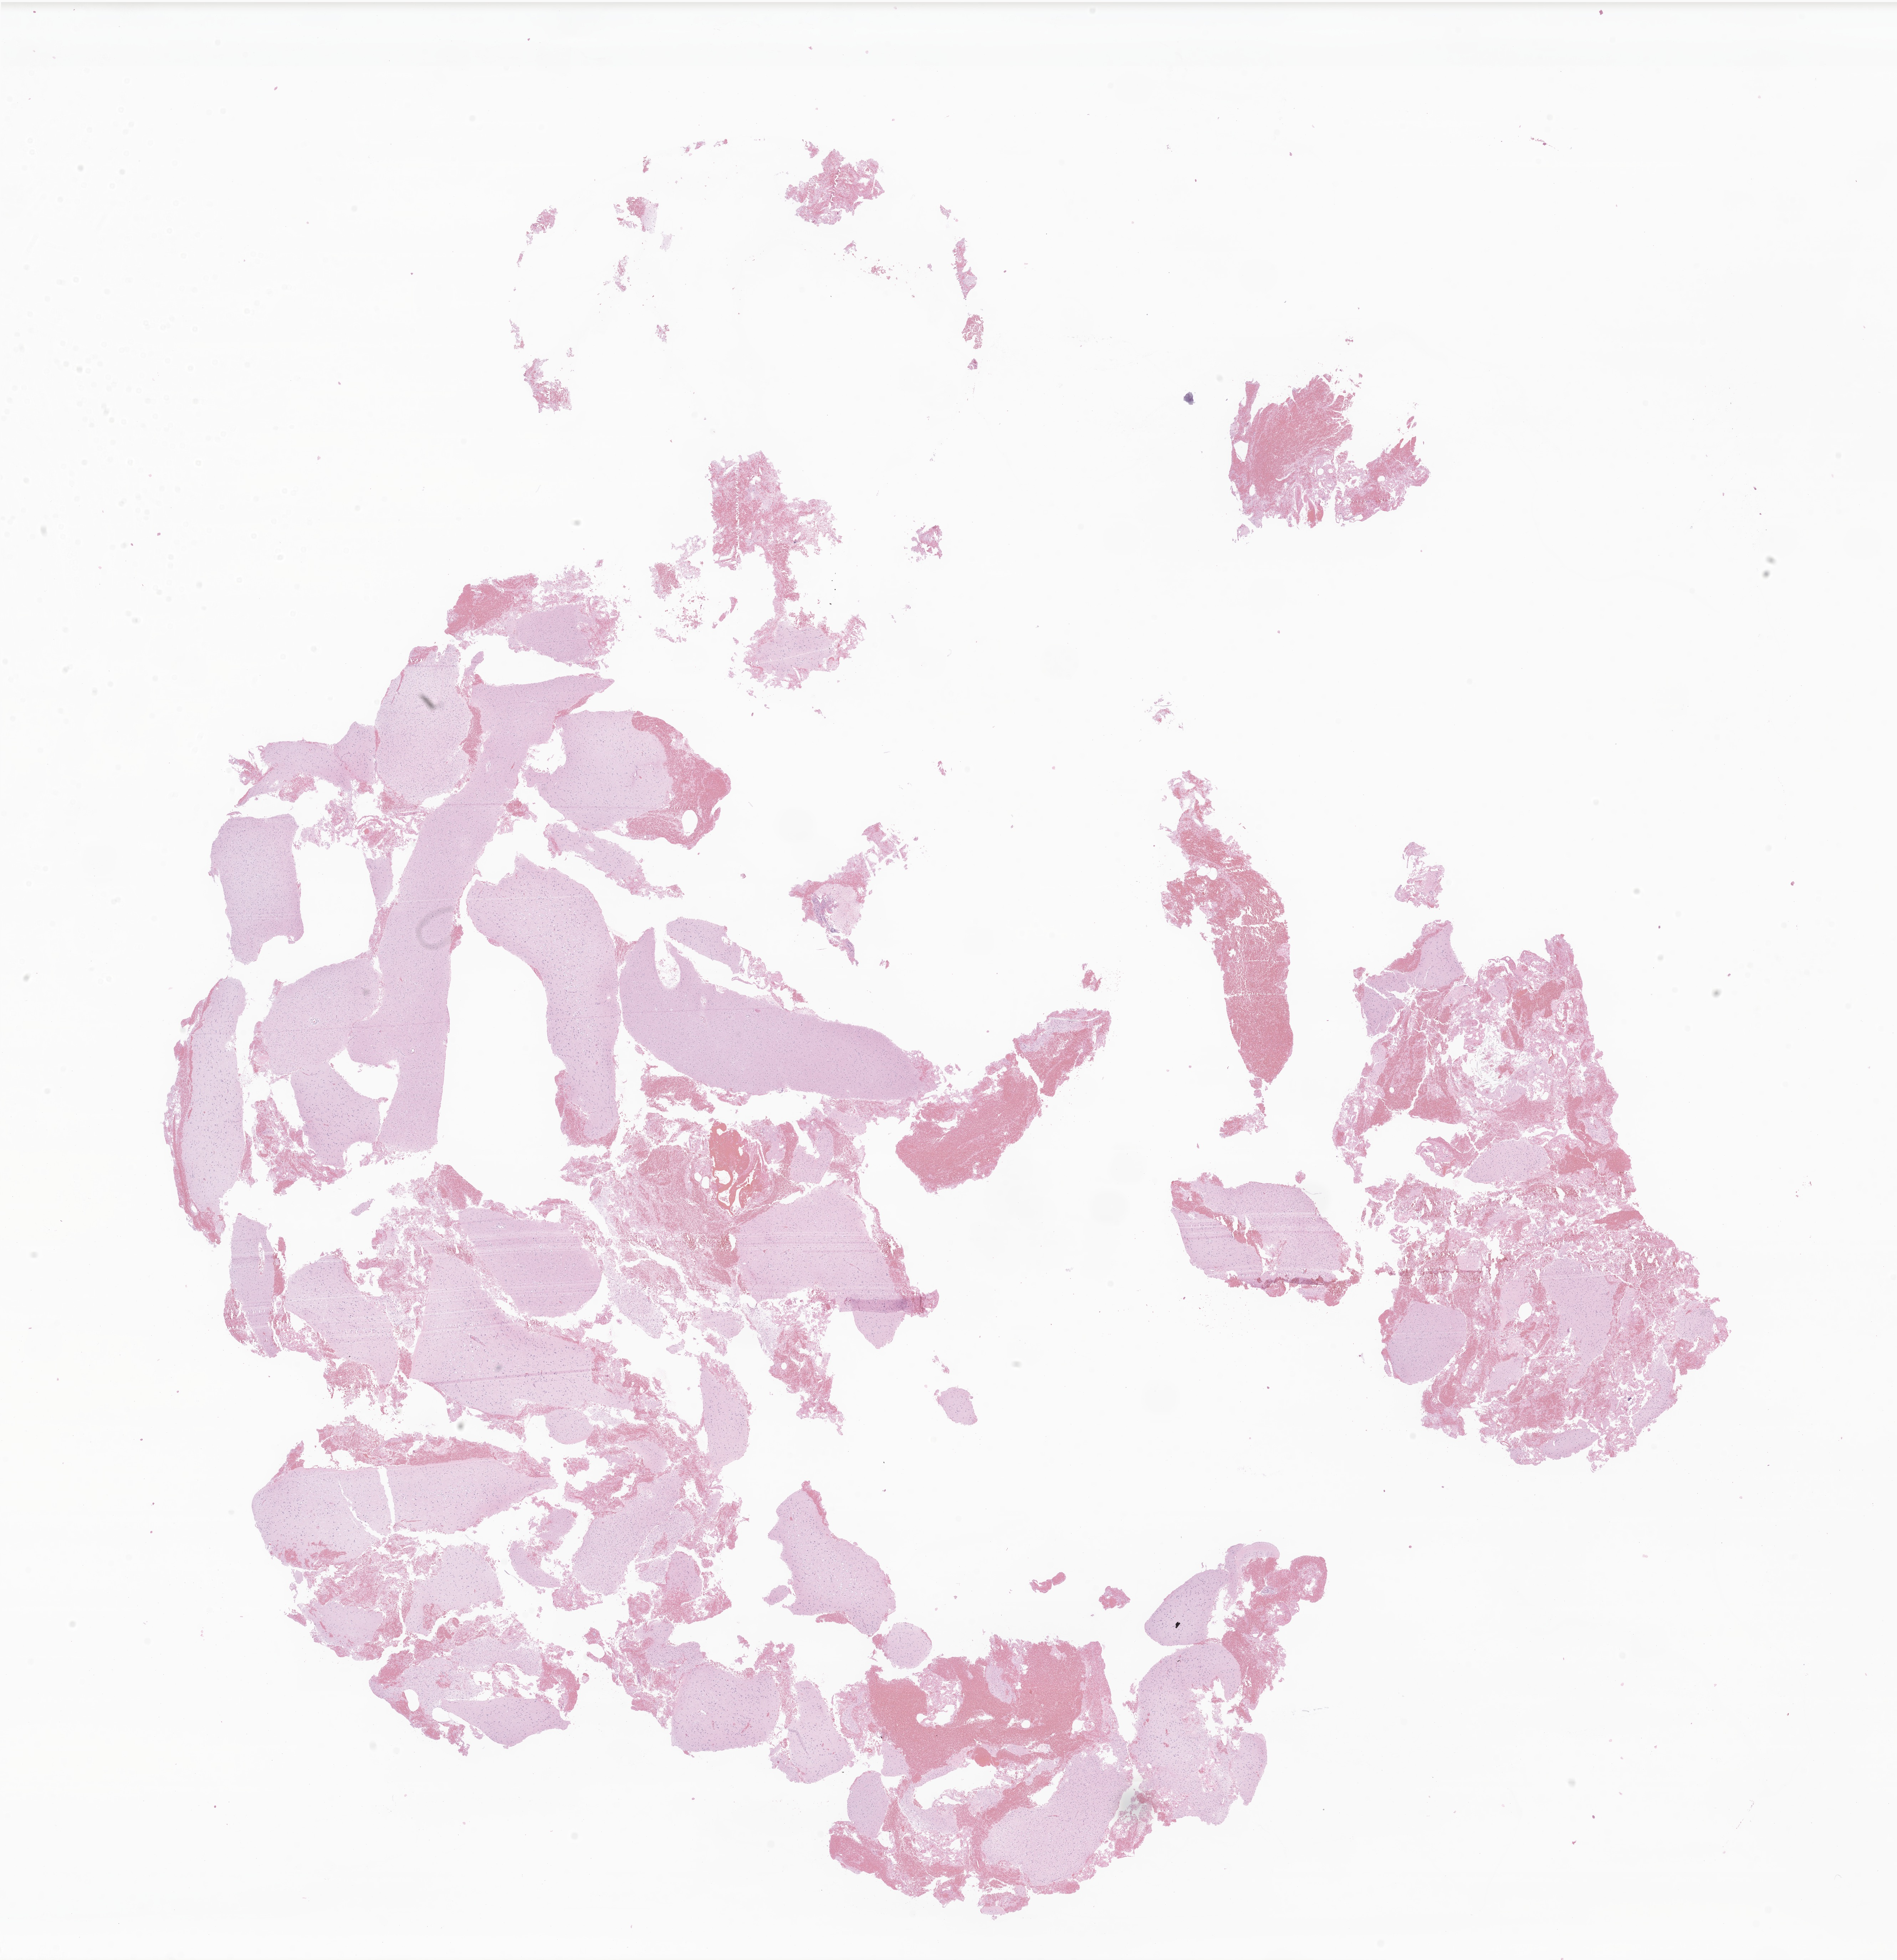
Digitized hematoxylin and eosin (H&E)-stained section of tumor tissue from the brain, whole scanned area (about 22.4 x 23.2 mm) shown as a low-resolution overview. FFPE section. Male patient, age 231 months (19 years 3 months).
Diagnosis: Neoplasm, uncertain whether benign or malignant.